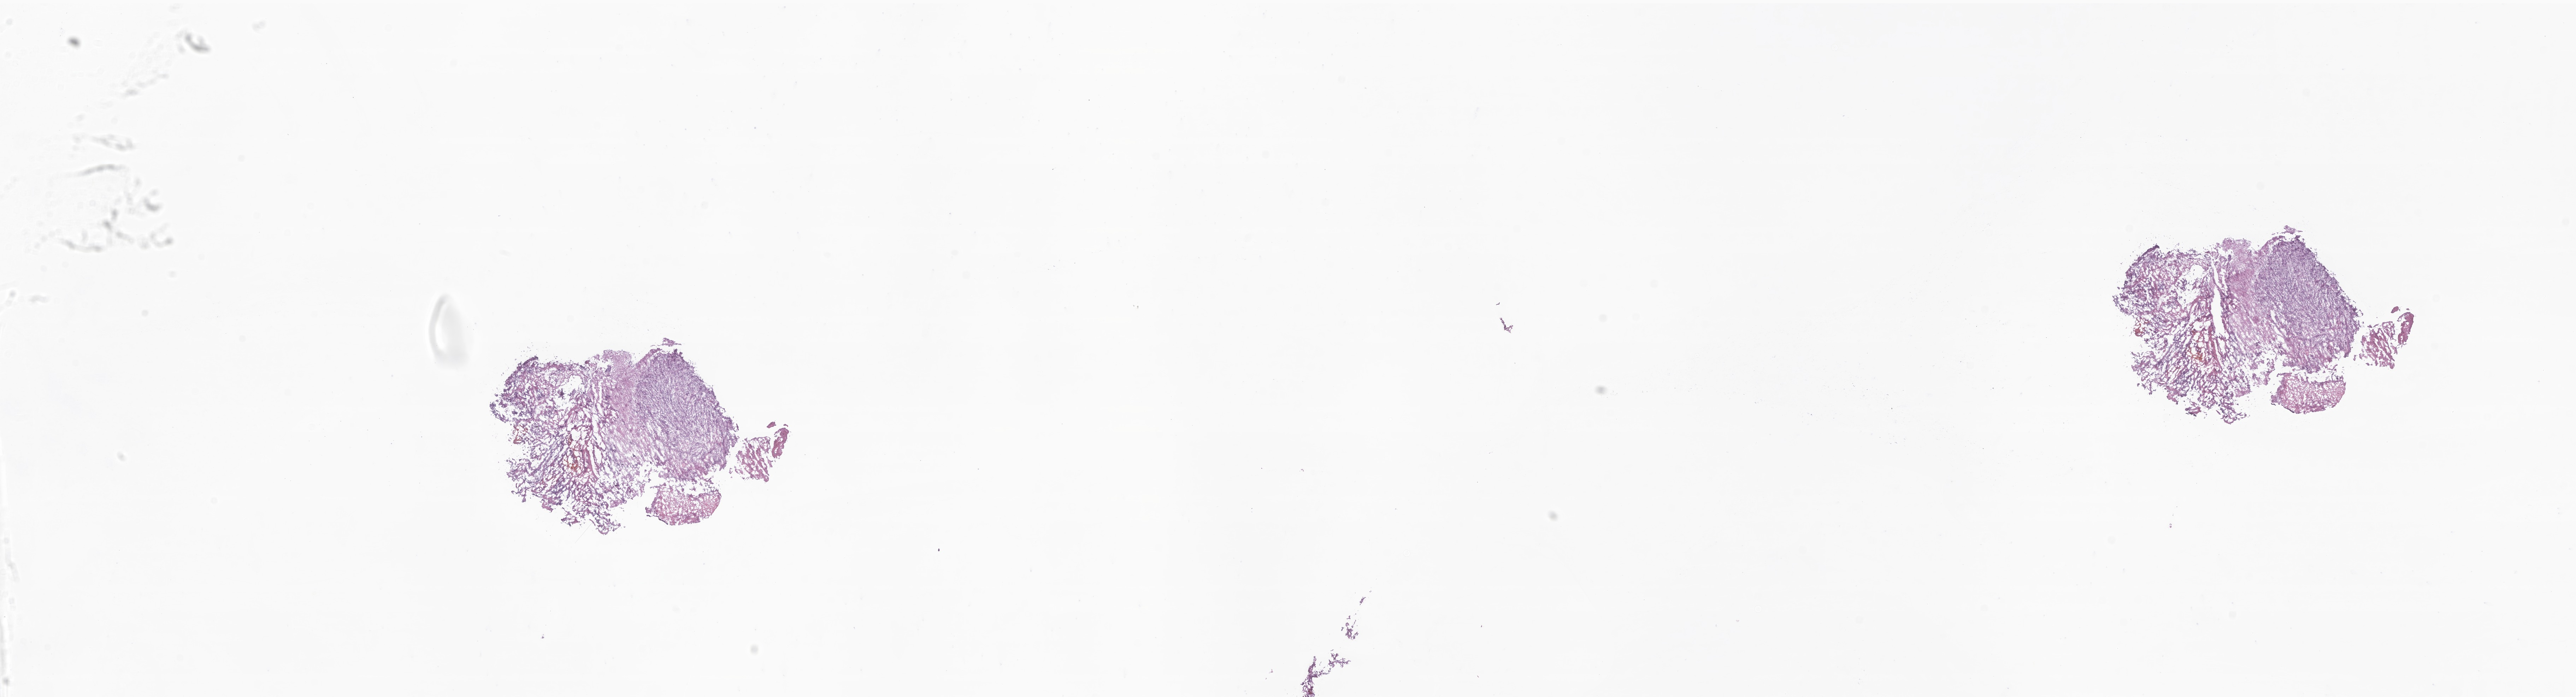
Whole-slide image, haematoxylin and eosin stain of tumor tissue from the brain, shown as a low-resolution overview of the whole scanned area (about 30.7 x 8.3 mm). Frozen section (OCT-embedded). Patient female; age 53 months.
• diagnosis (ICD-O-3 morphology term): Atypical teratoid/rhabdoid tumor